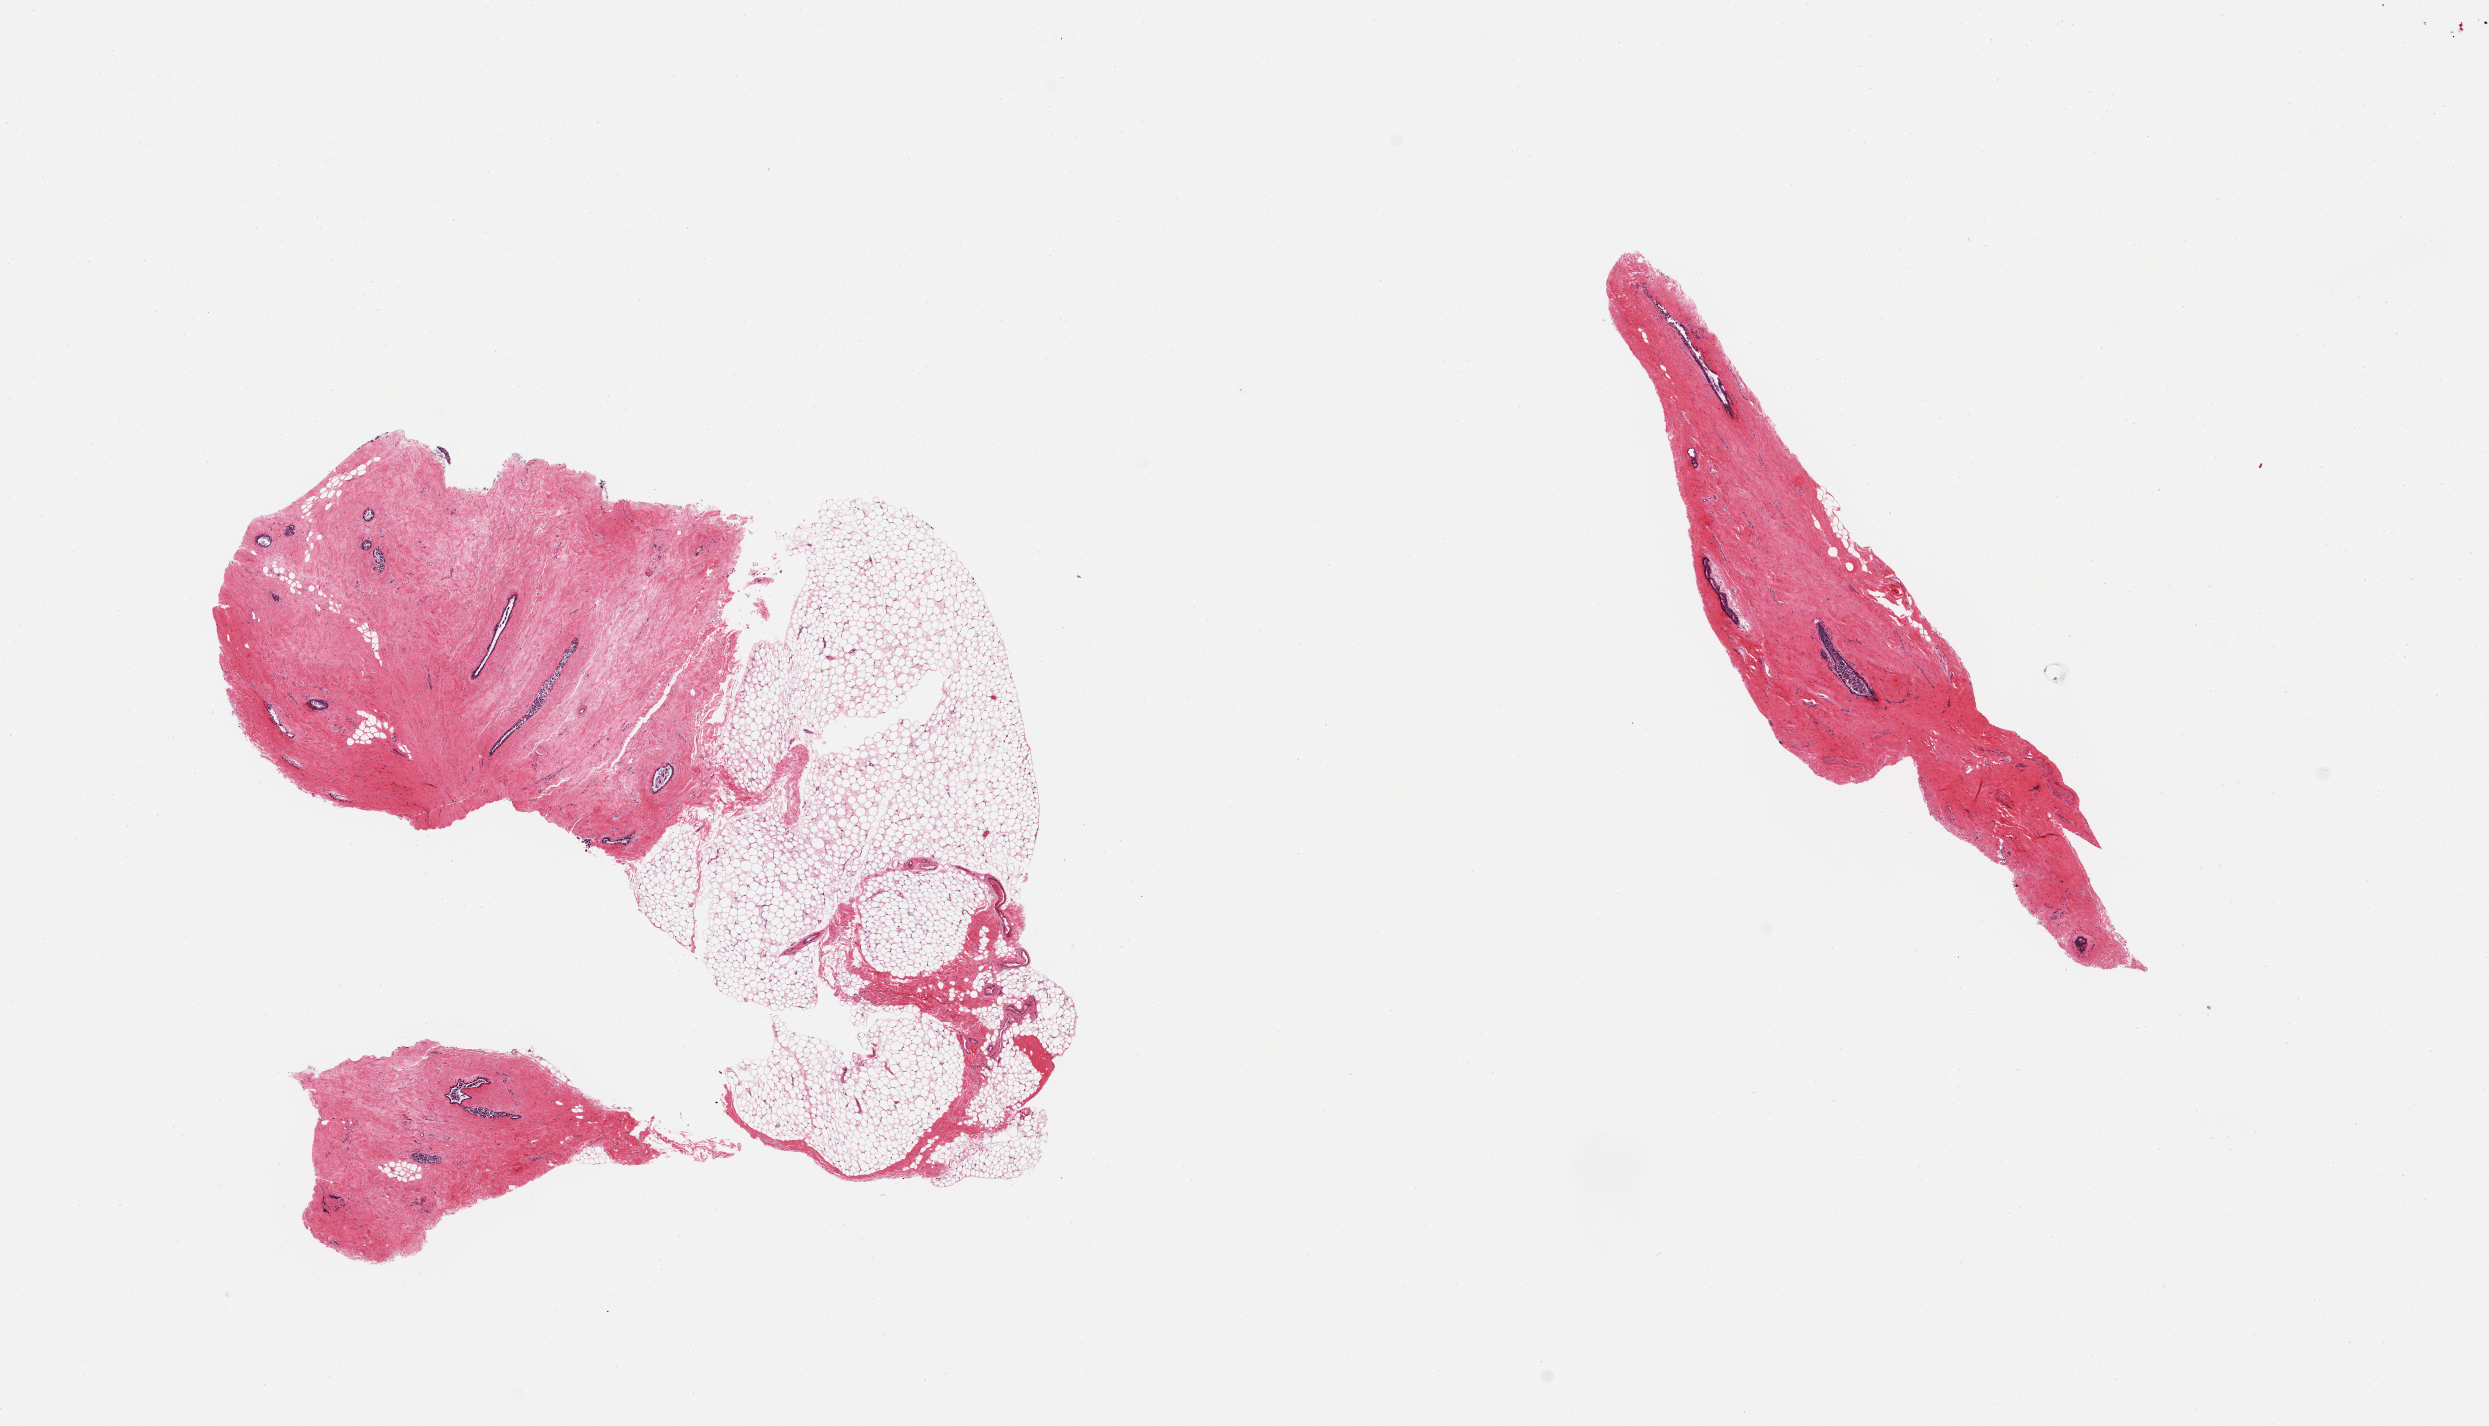
Digitized H&E-stained section — a low-resolution overview of the entire scanned area, about 19.7 x 11.3 mm; PAXgene-fixed paraffin-embedded (PFPE) section; section of breast (target tissue); donor tissue sample. Donor: male.
Reviewer comment on this tissue sample: 2 pieces; one piece is 5-% fat and 5-% stroma with ducts with sloughing epithelium, second is essentially entirely stroma/ducts.